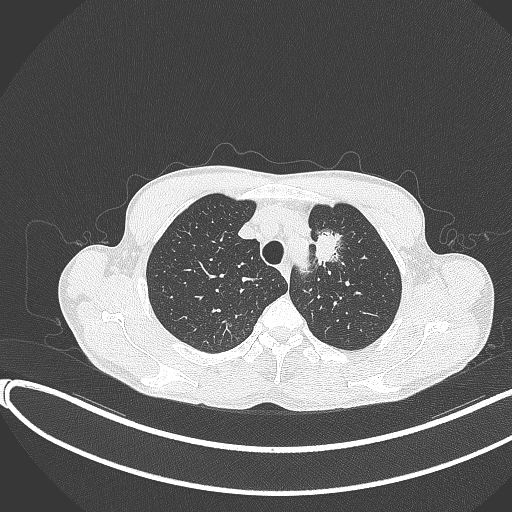
Chest CT, one axial slice. Slice 311 of 374 in the series (ordered by position). Reconstruction kernel B70f. 120 kVp. Lung window (W 1500 / L -600 HU). 1 mm slice thickness. 512 × 512 image matrix, field of view 400 × 400 mm. Male patient, age 58 years. From the clinical record (not read from this slice): clinical TNM (as recorded): T1c N1 M0.
Outlined on this slice (rectangle marked by the reading radiologist):
- lung tumour (recorded histology: adenocarcinoma): bounding box (x1, y1, x2, y2) in pixels: (313, 224, 354, 278)